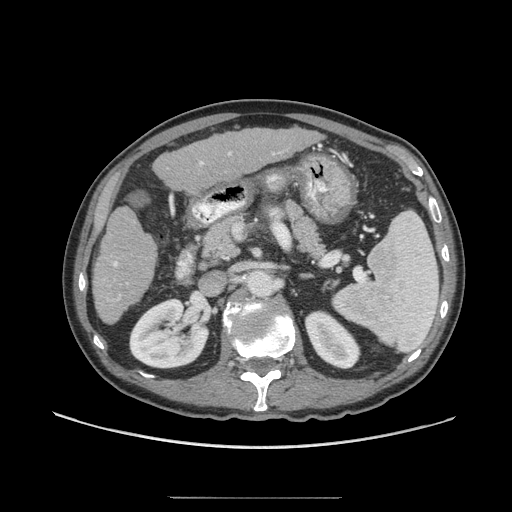
Contrast-enhanced abdominal CT (liver protocol), one axial slice; position 27 of 71 along the scan axis; soft-tissue window (W 400 / L 40 HU); 2.5 mm slice thickness; 512 × 512 image matrix, field of view 400 × 400 mm. From the clinical record (not read from this slice): diagnosis: hepatocellular carcinoma (patient treated with transarterial chemoembolisation; whether this scan precedes or follows treatment is not stated here); TNM stage (as recorded): Stage-I; Child-Pugh class: A; tumour nodularity: uninodular; tumour size: 3.5 cm.
Structures marked on this image (semi-automatically segmented with operator editing):
- liver parenchyma outside the tumour (the mass and vessels are separate outlines, so this box may not span the whole liver): bounding box <92,128,314,324> (left, top, right, bottom; pixels)
- liver vessels: <113,153,275,300>